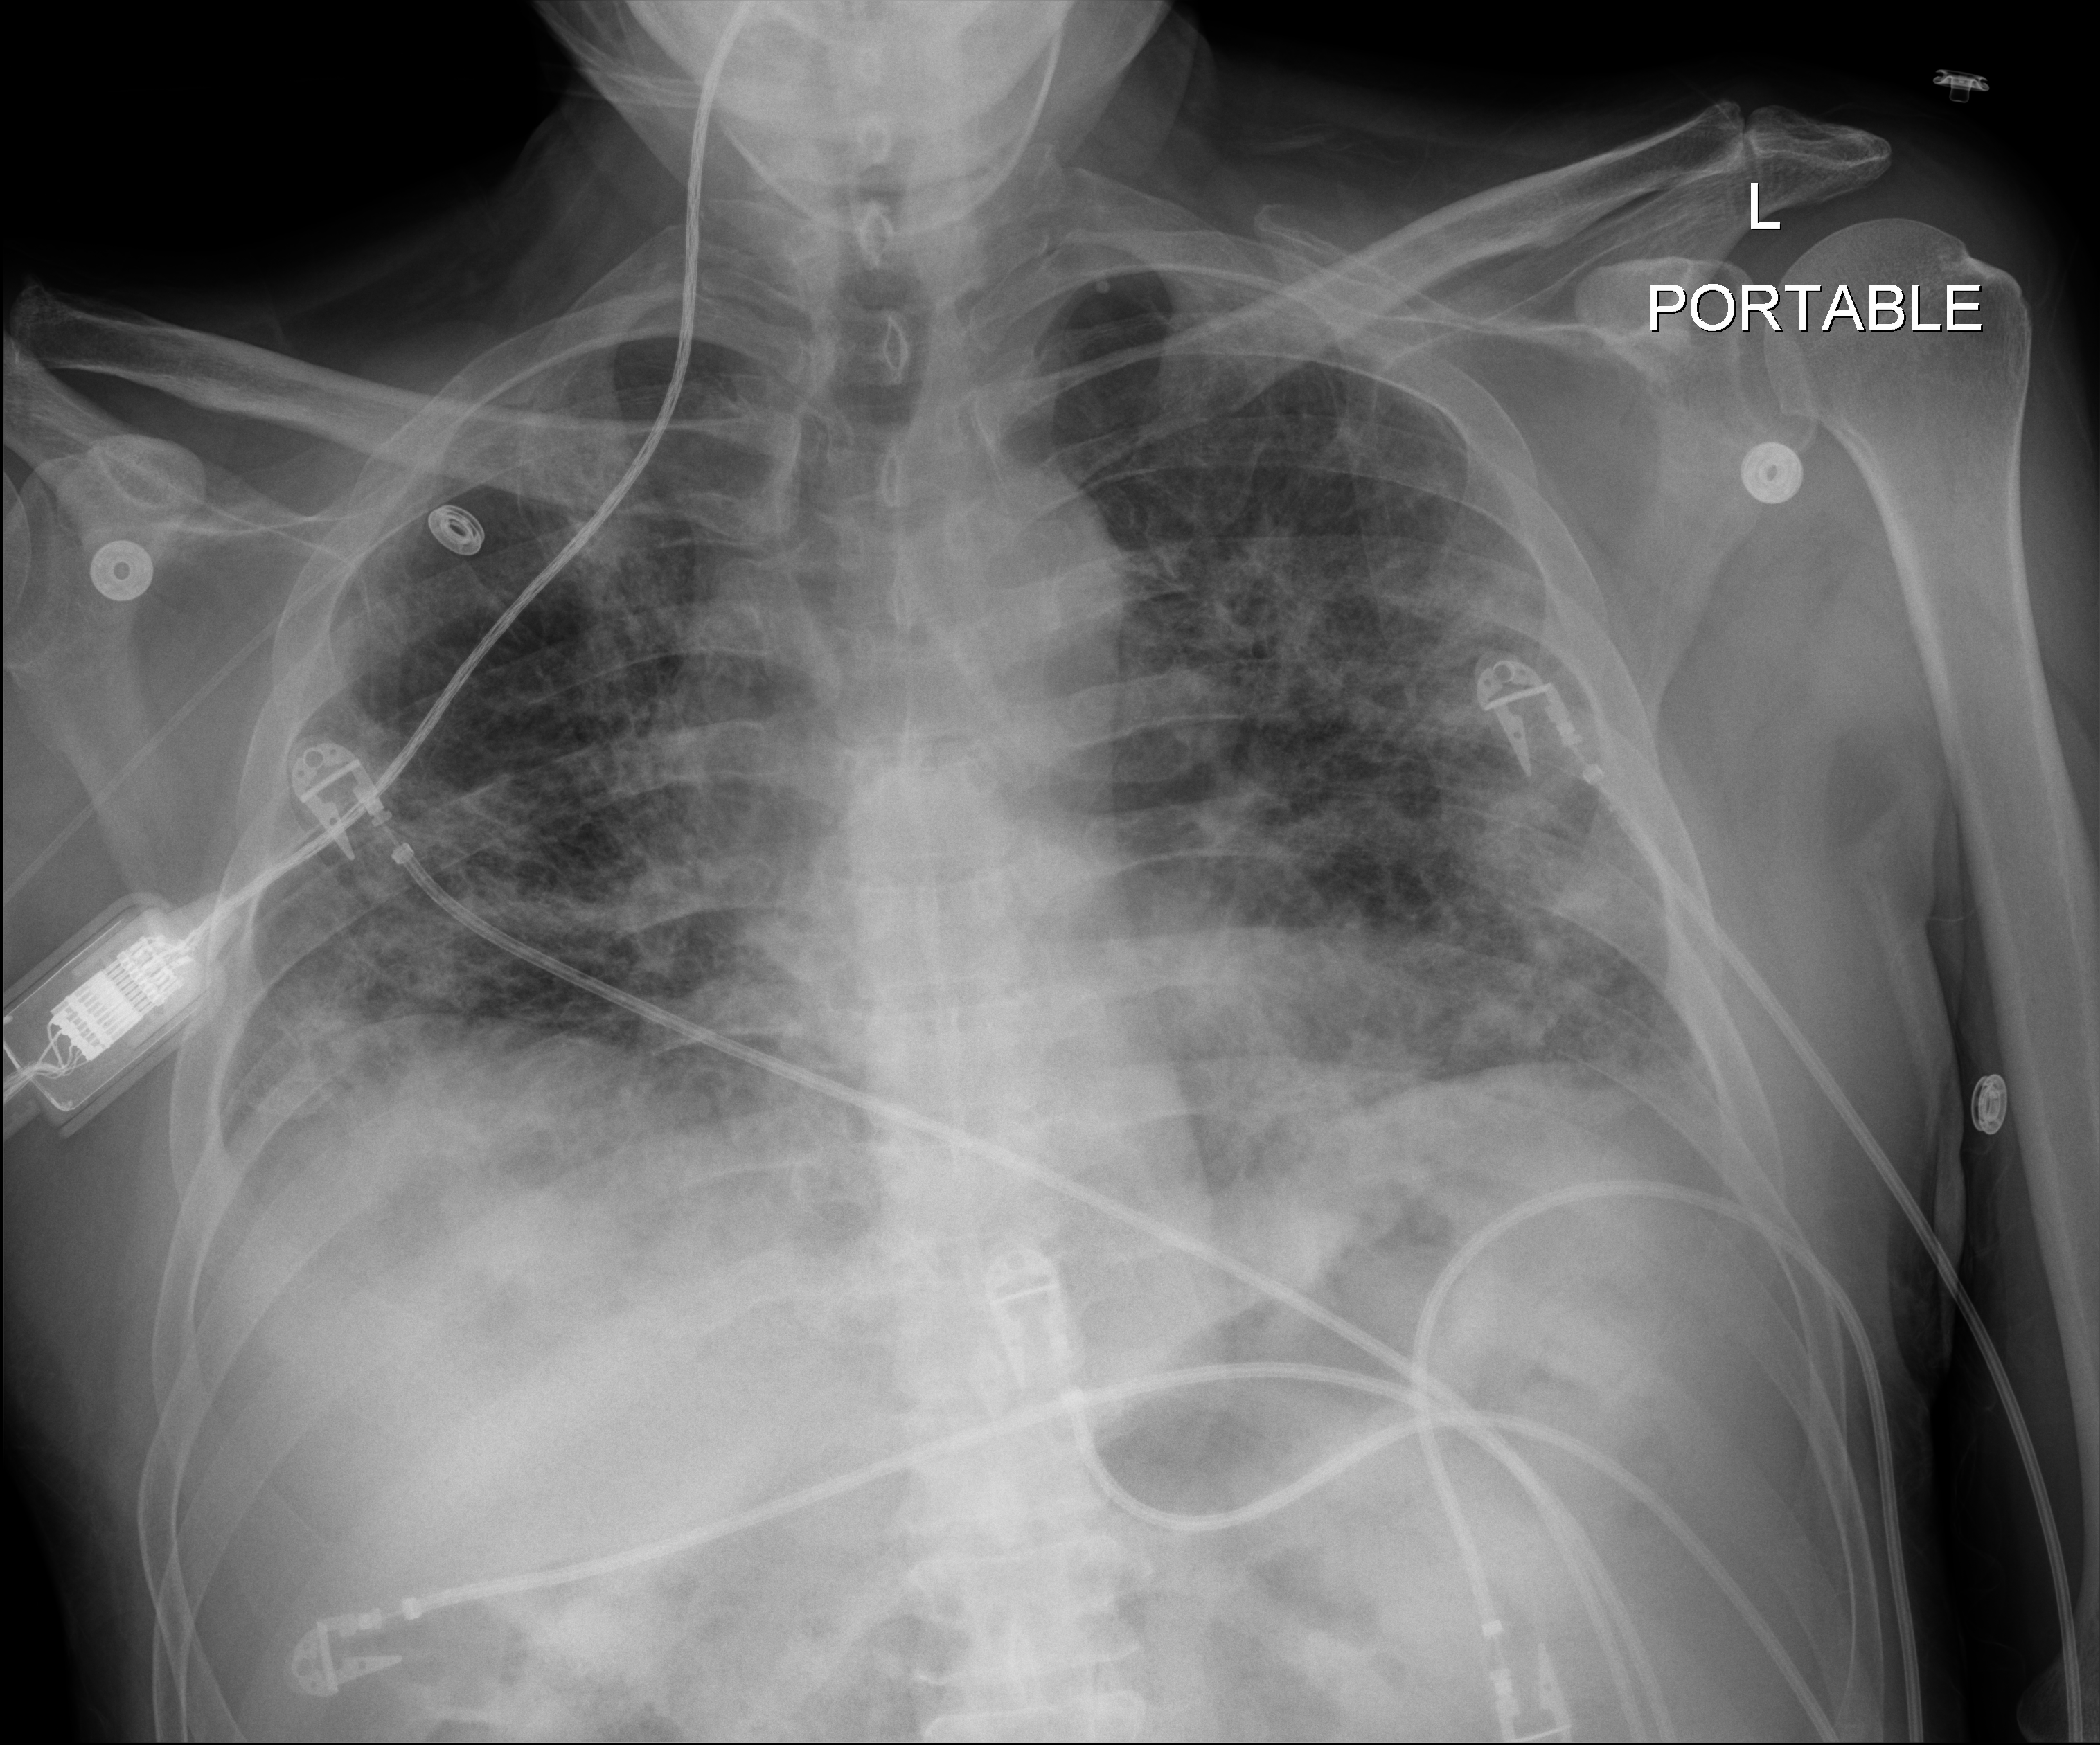
Bedside chest radiograph (digital radiography), anteroposterior (AP) projection. Male patient hospitalised with COVID-19, age 18–59 years.
Hospital-stay facts (about this admission, not read from this image; timing relative to this image not recorded): admitted to intensive care during this hospital stay: yes; mechanically ventilated during this hospital stay: yes.